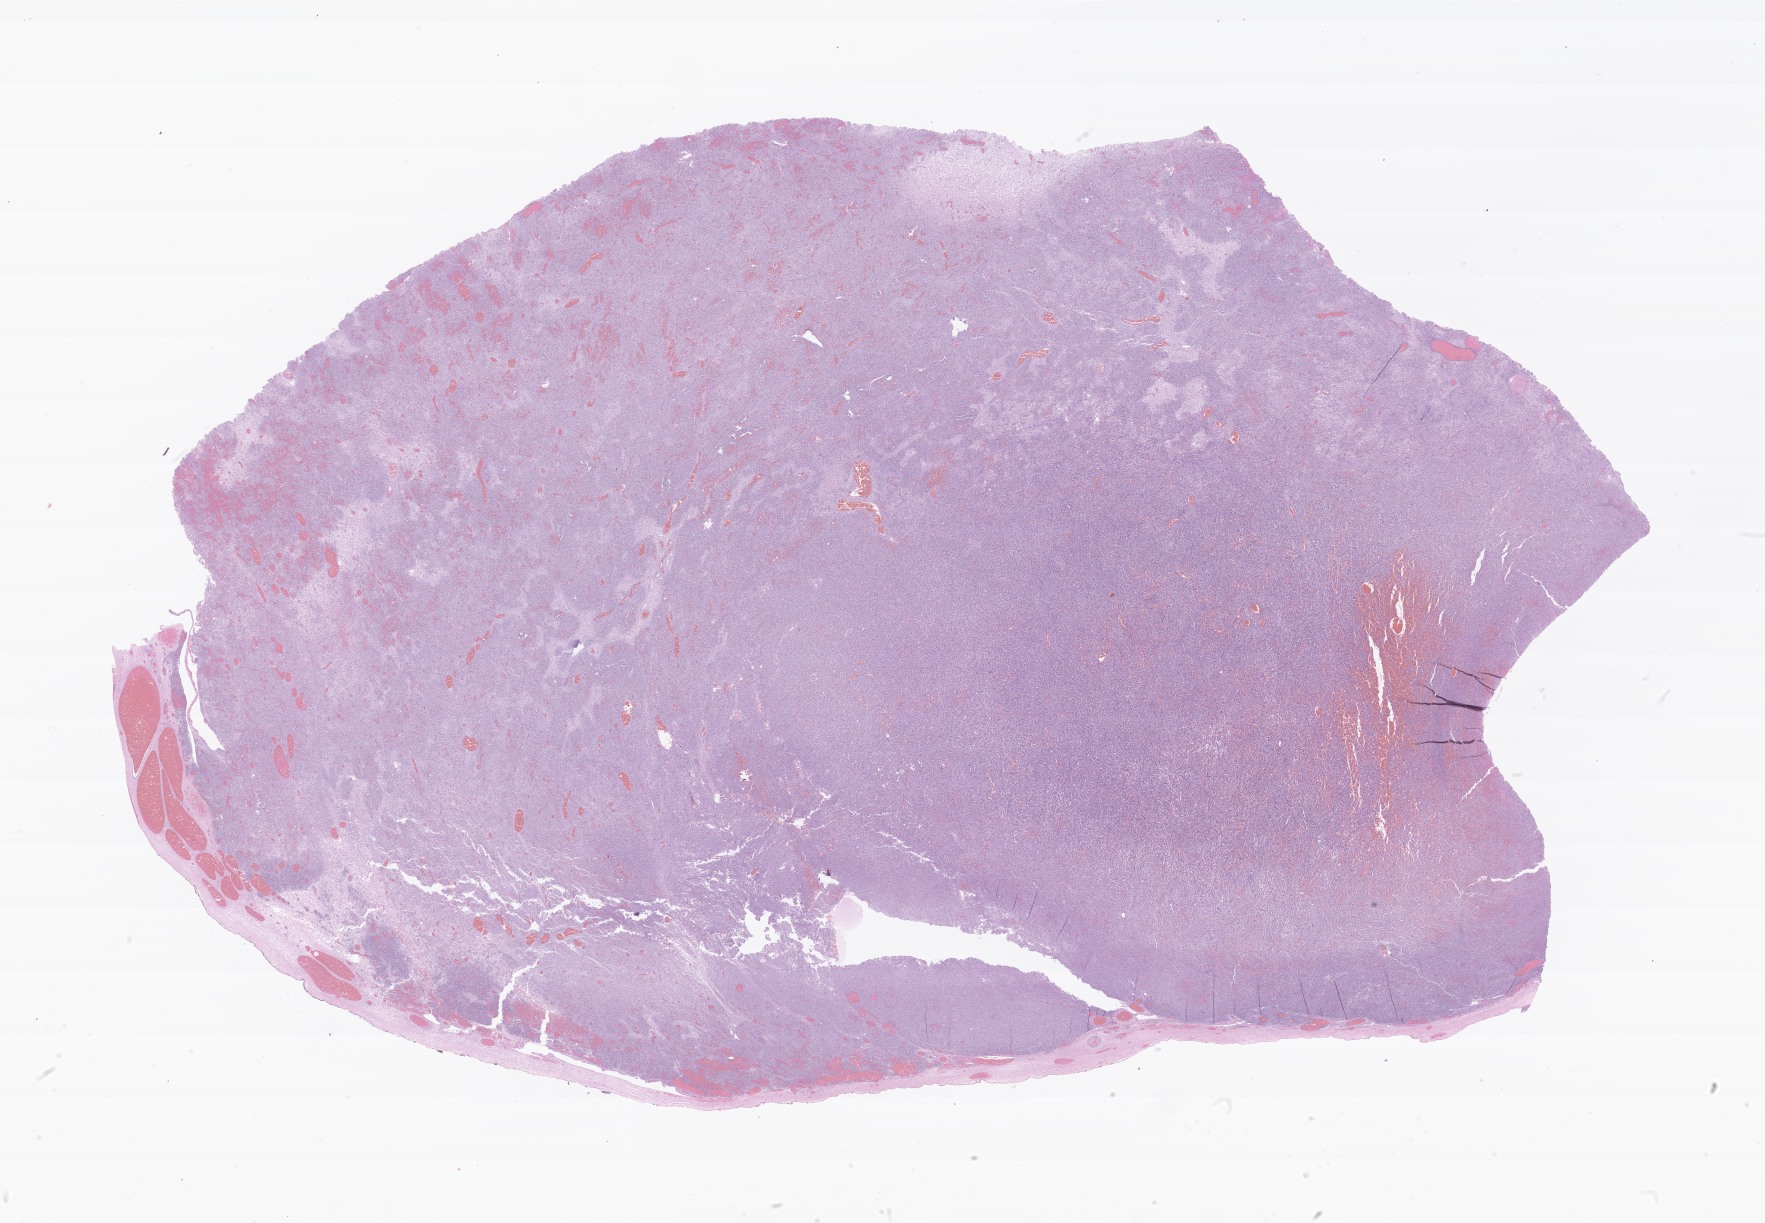
Hematoxylin and eosin (H&E) whole-slide image of tumor tissue from the ovary — whole scanned area (about 29.7 x 20.6 mm) shown as a low-resolution overview, FFPE section. Patient: female, age 180 months (15 years).
• diagnosis: Sertoli cell tumor, NOS